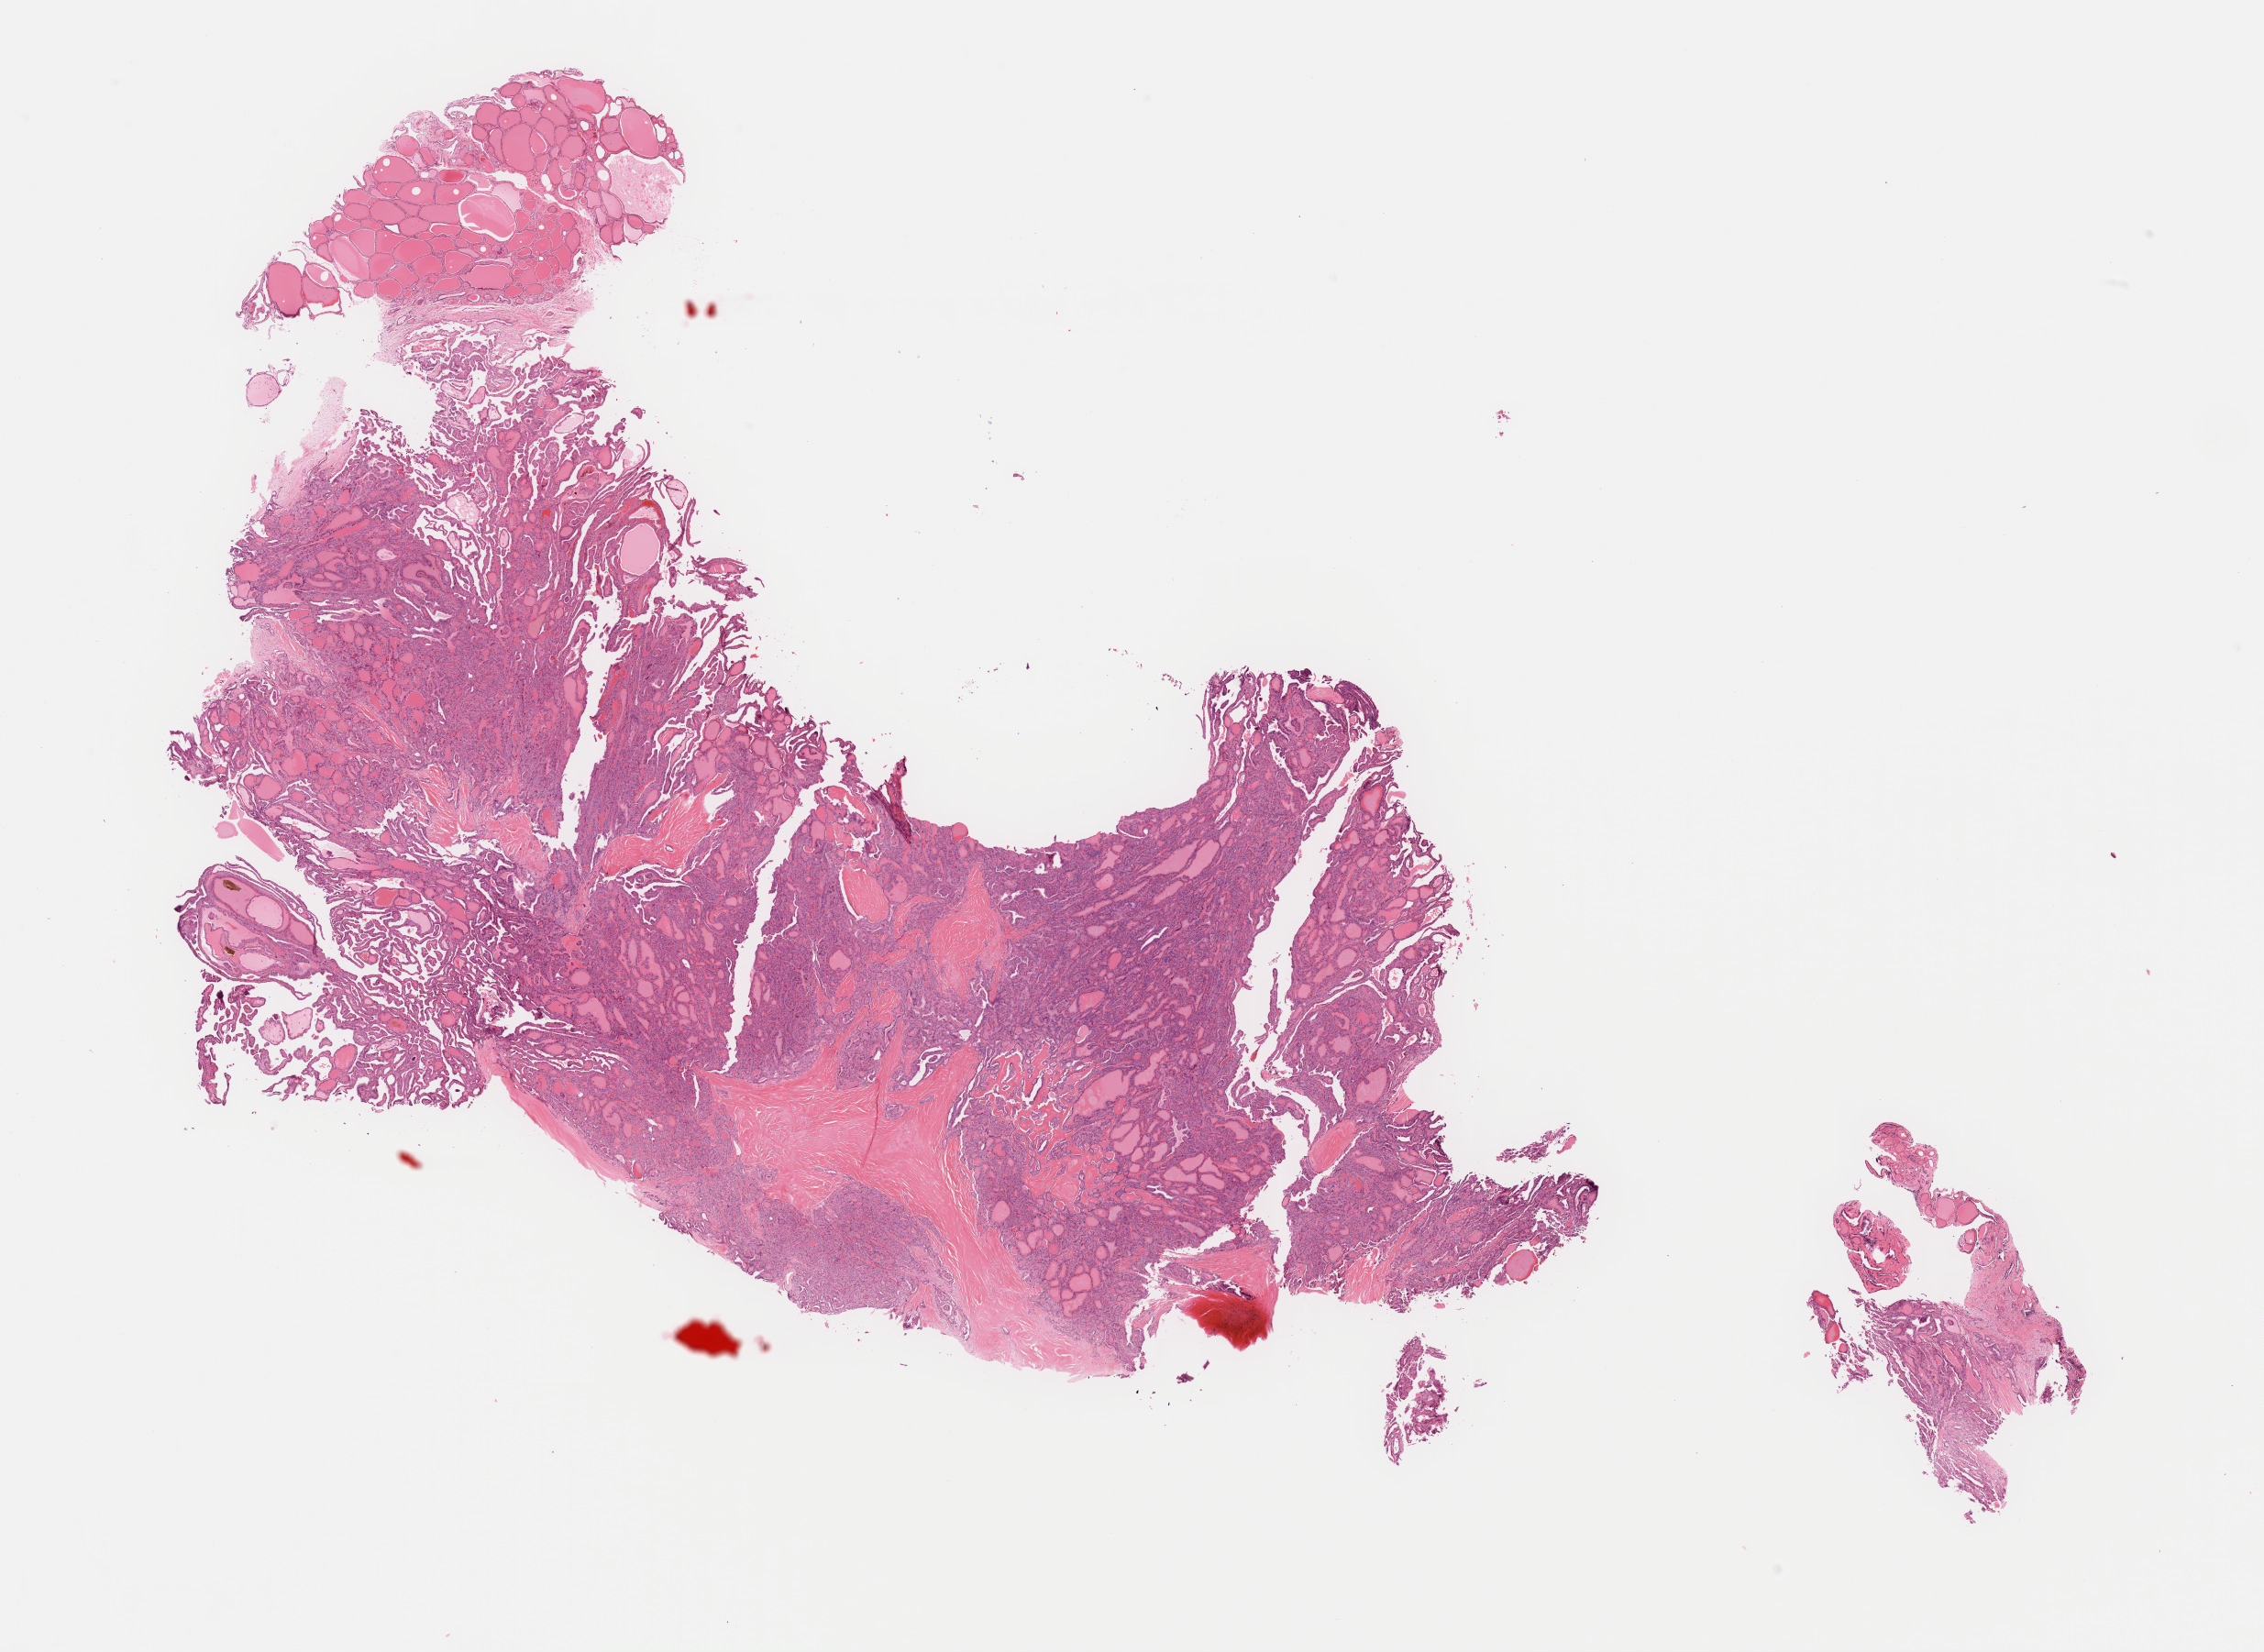
Digitized H&E-stained tissue section (whole slide), shown as a low-resolution overview of the whole scanned area (about 19.5 x 14.2 mm). Formalin-fixed paraffin-embedded (FFPE) diagnostic section. Primary tumour sample from the thyroid. Patient: female, age at initial diagnosis 57 years.
TNM: TX NX M0. Diagnosis: Papillary adenocarcinoma, NOS (thyroid gland). Laterality: right. AJCC pathologic stage: I (7th edition).